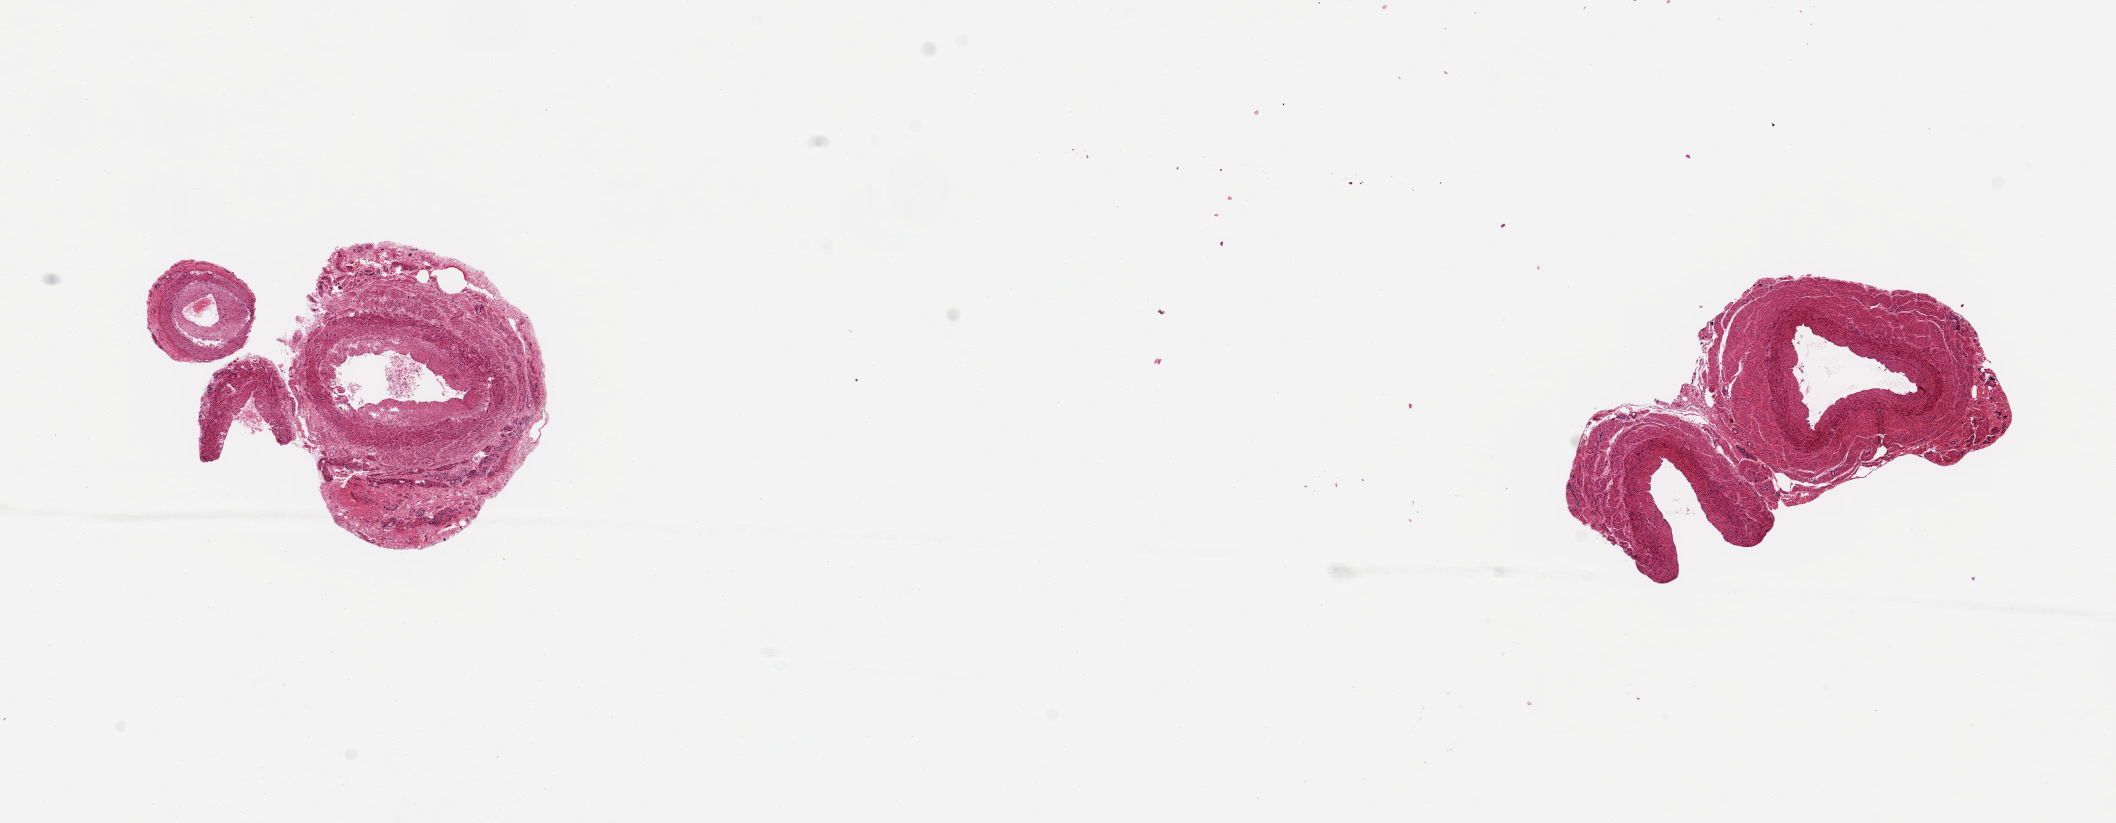
Whole-slide image, haematoxylin and eosin stain, whole scanned area (about 16.7 x 6.5 mm) shown as a low-resolution overview; PAXgene-fixed, paraffin-embedded tissue; sampled site (target tissue): fallopian tube; donor tissue sample.
Reviewer comment on this tissue sample: Not fallopian tube, small artery.